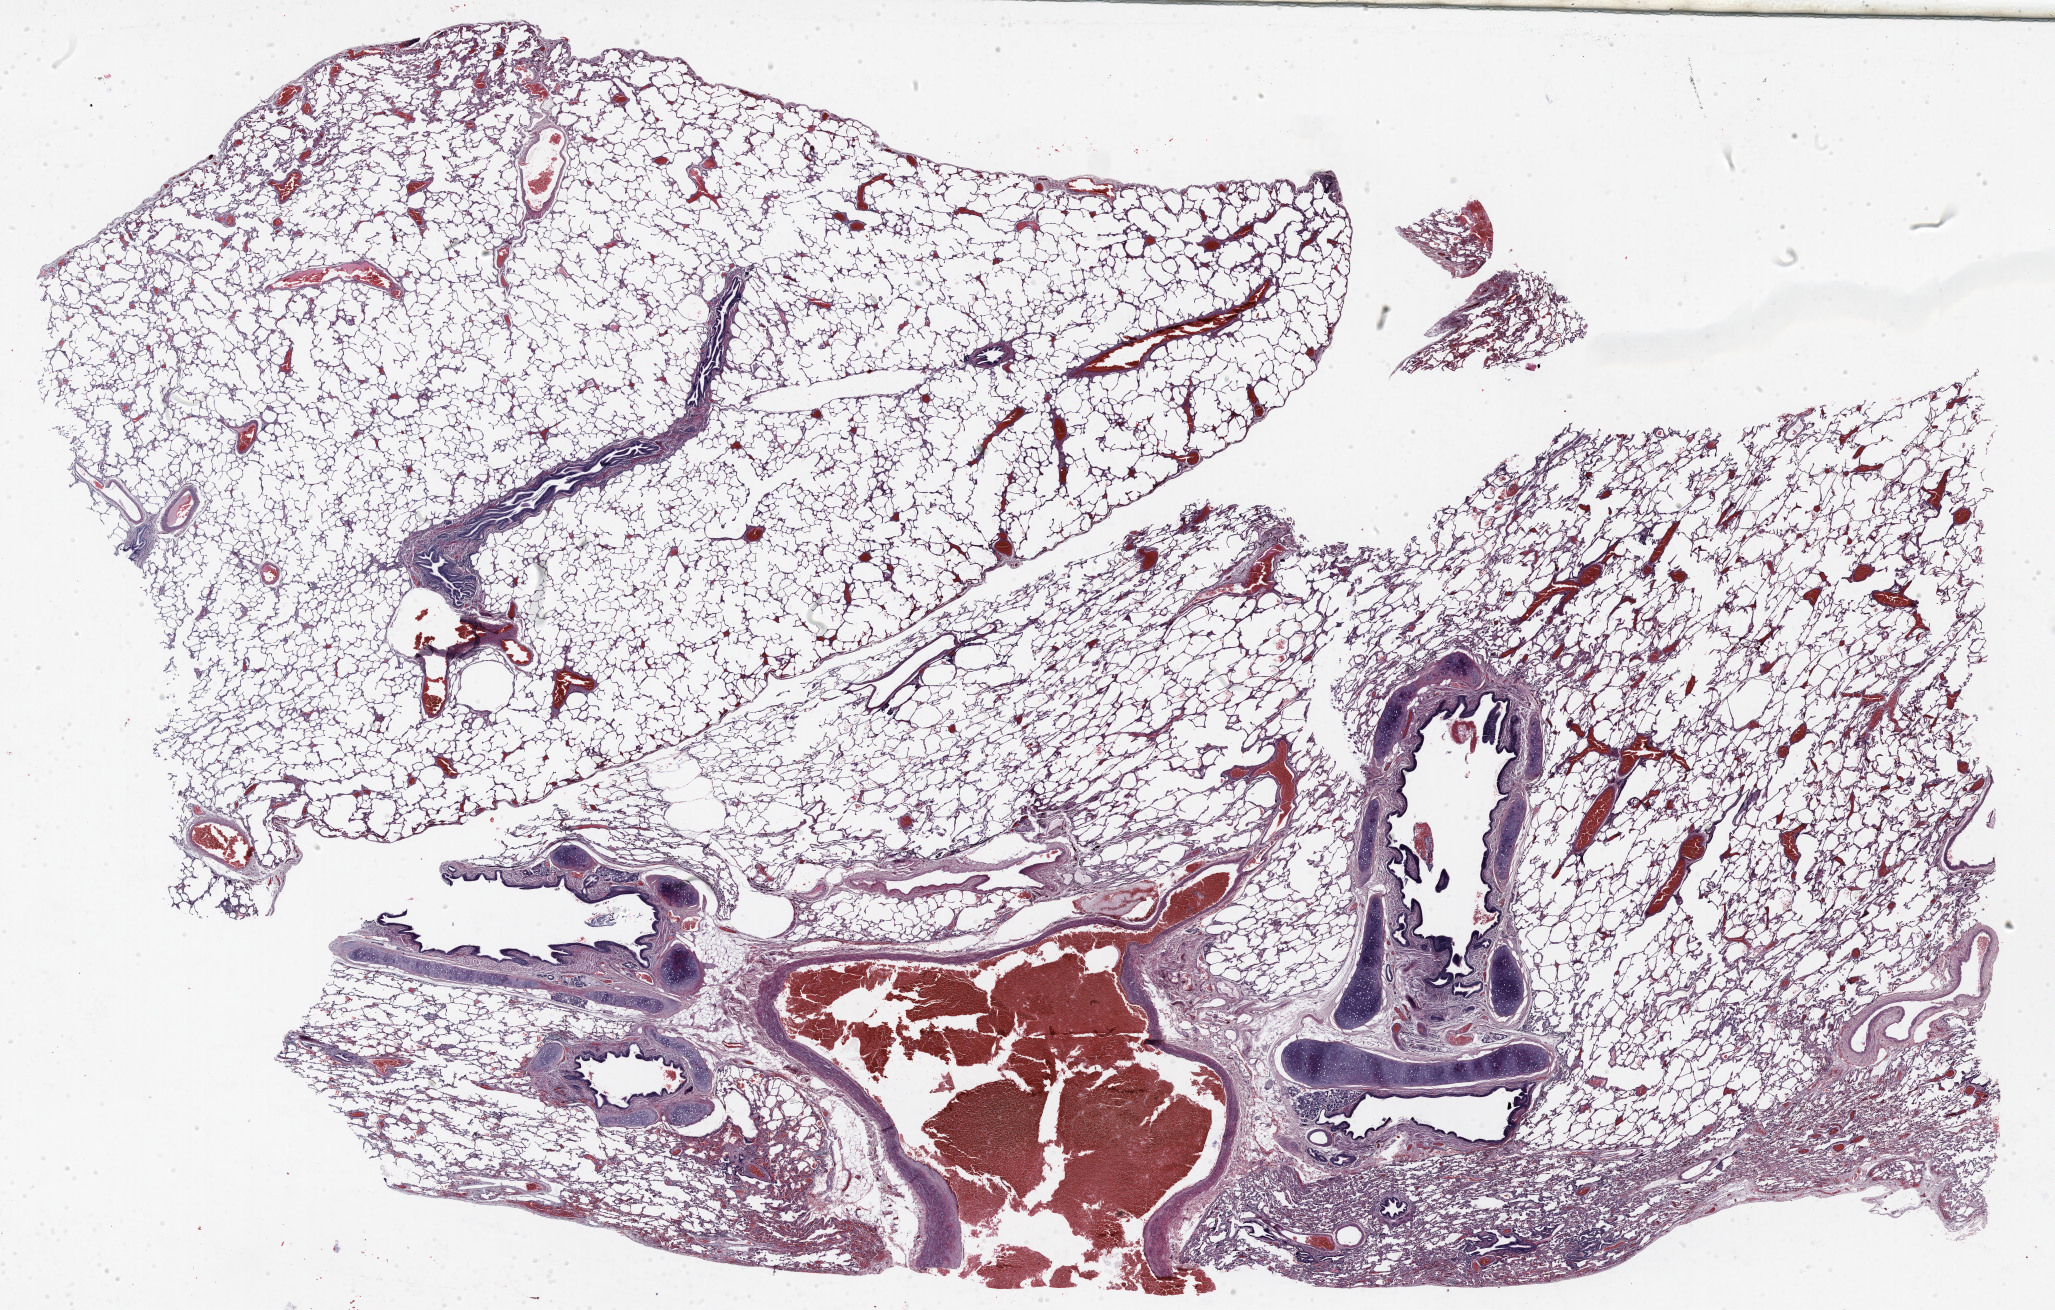
Hematoxylin and eosin (H&E) stained whole-slide image — a low-resolution overview of the entire scanned area, about 33.0 x 21.1 mm (from a 20x scan); FFPE section; lung tissue. Male patient, aged 62 at enrolment. Current smoker at enrolment. Grade: moderately differentiated (G2).
Stage (AJCC 6th edition): IA. Tumour size (pathology): 30 mm. Primary tumour location (clinical record): left lower lobe. Participant's lung-cancer diagnosis: Adenocarcinoma, NOS (ICD-O-3 8140/3).